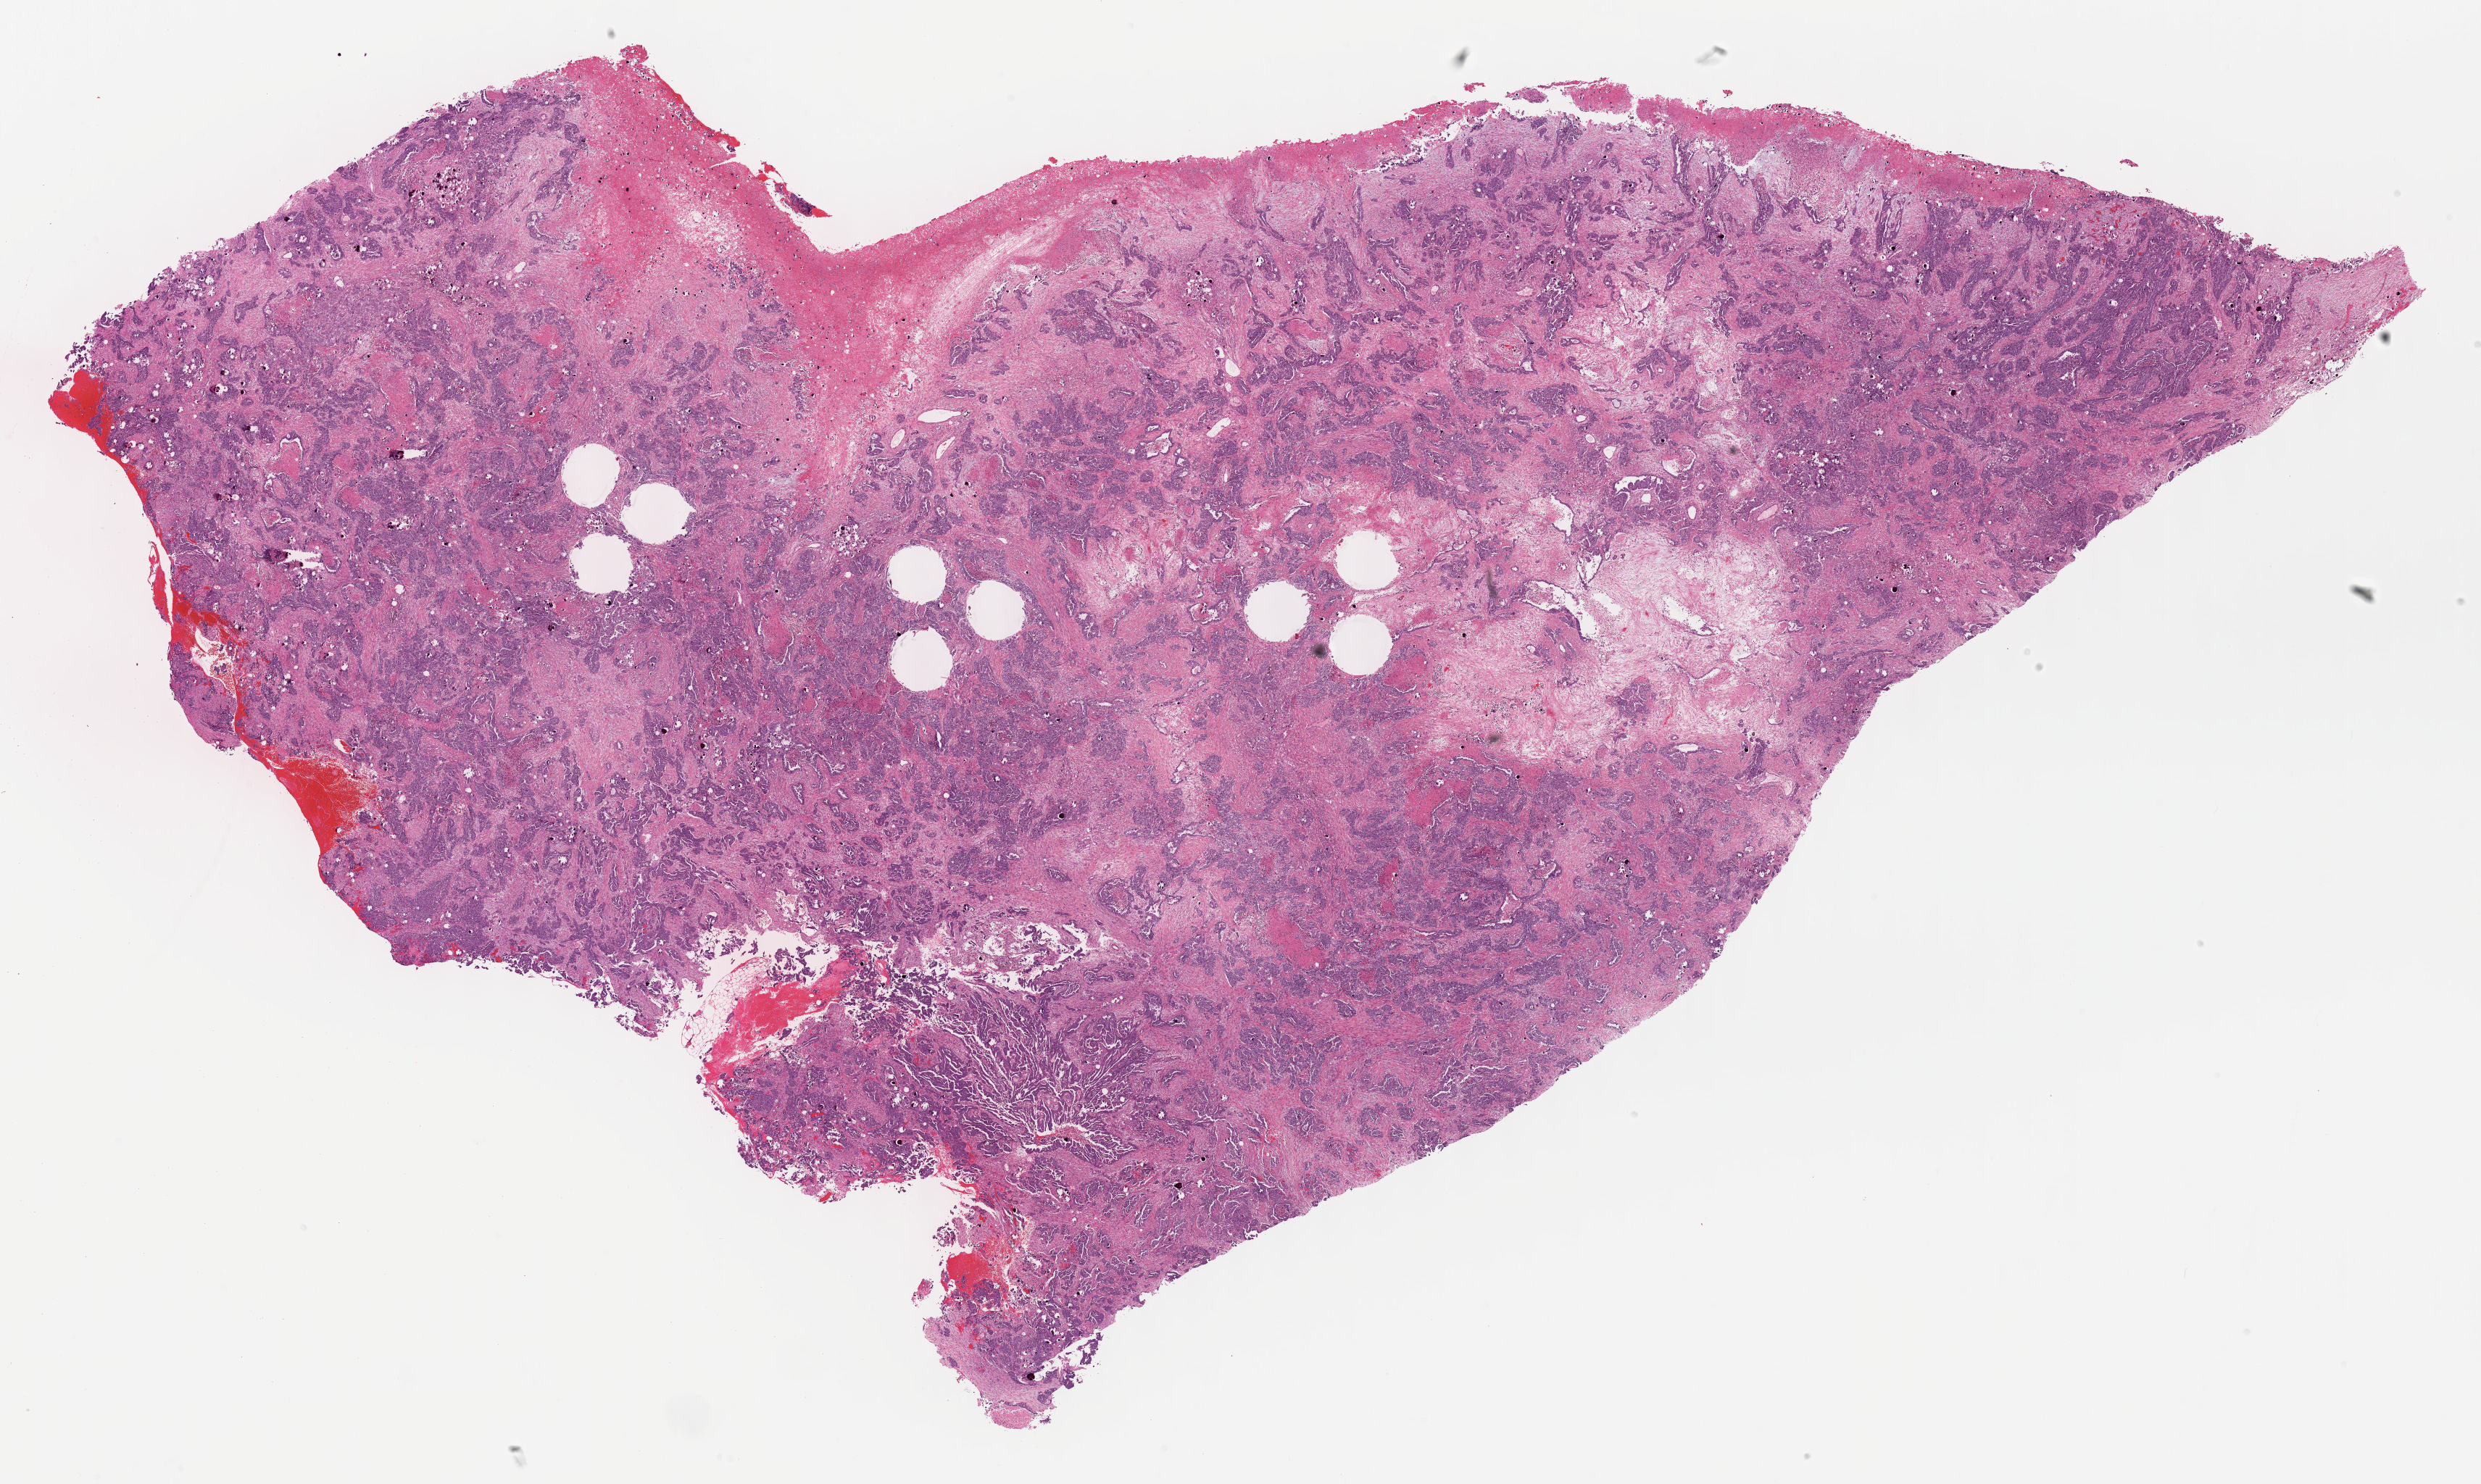
Whole-slide histology image, H&E-stained, low-resolution overview of the scanned area, about 27.7 x 16.6 mm (acquisition: 40x scan); formalin-fixed paraffin-embedded (FFPE) diagnostic section; ovary, primary tumour sample. Female patient; age at initial diagnosis 60 years. Histologic grade: G3 (poorly differentiated).
Histologic diagnosis: Serous cystadenocarcinoma, NOS. FIGO stage: IV.